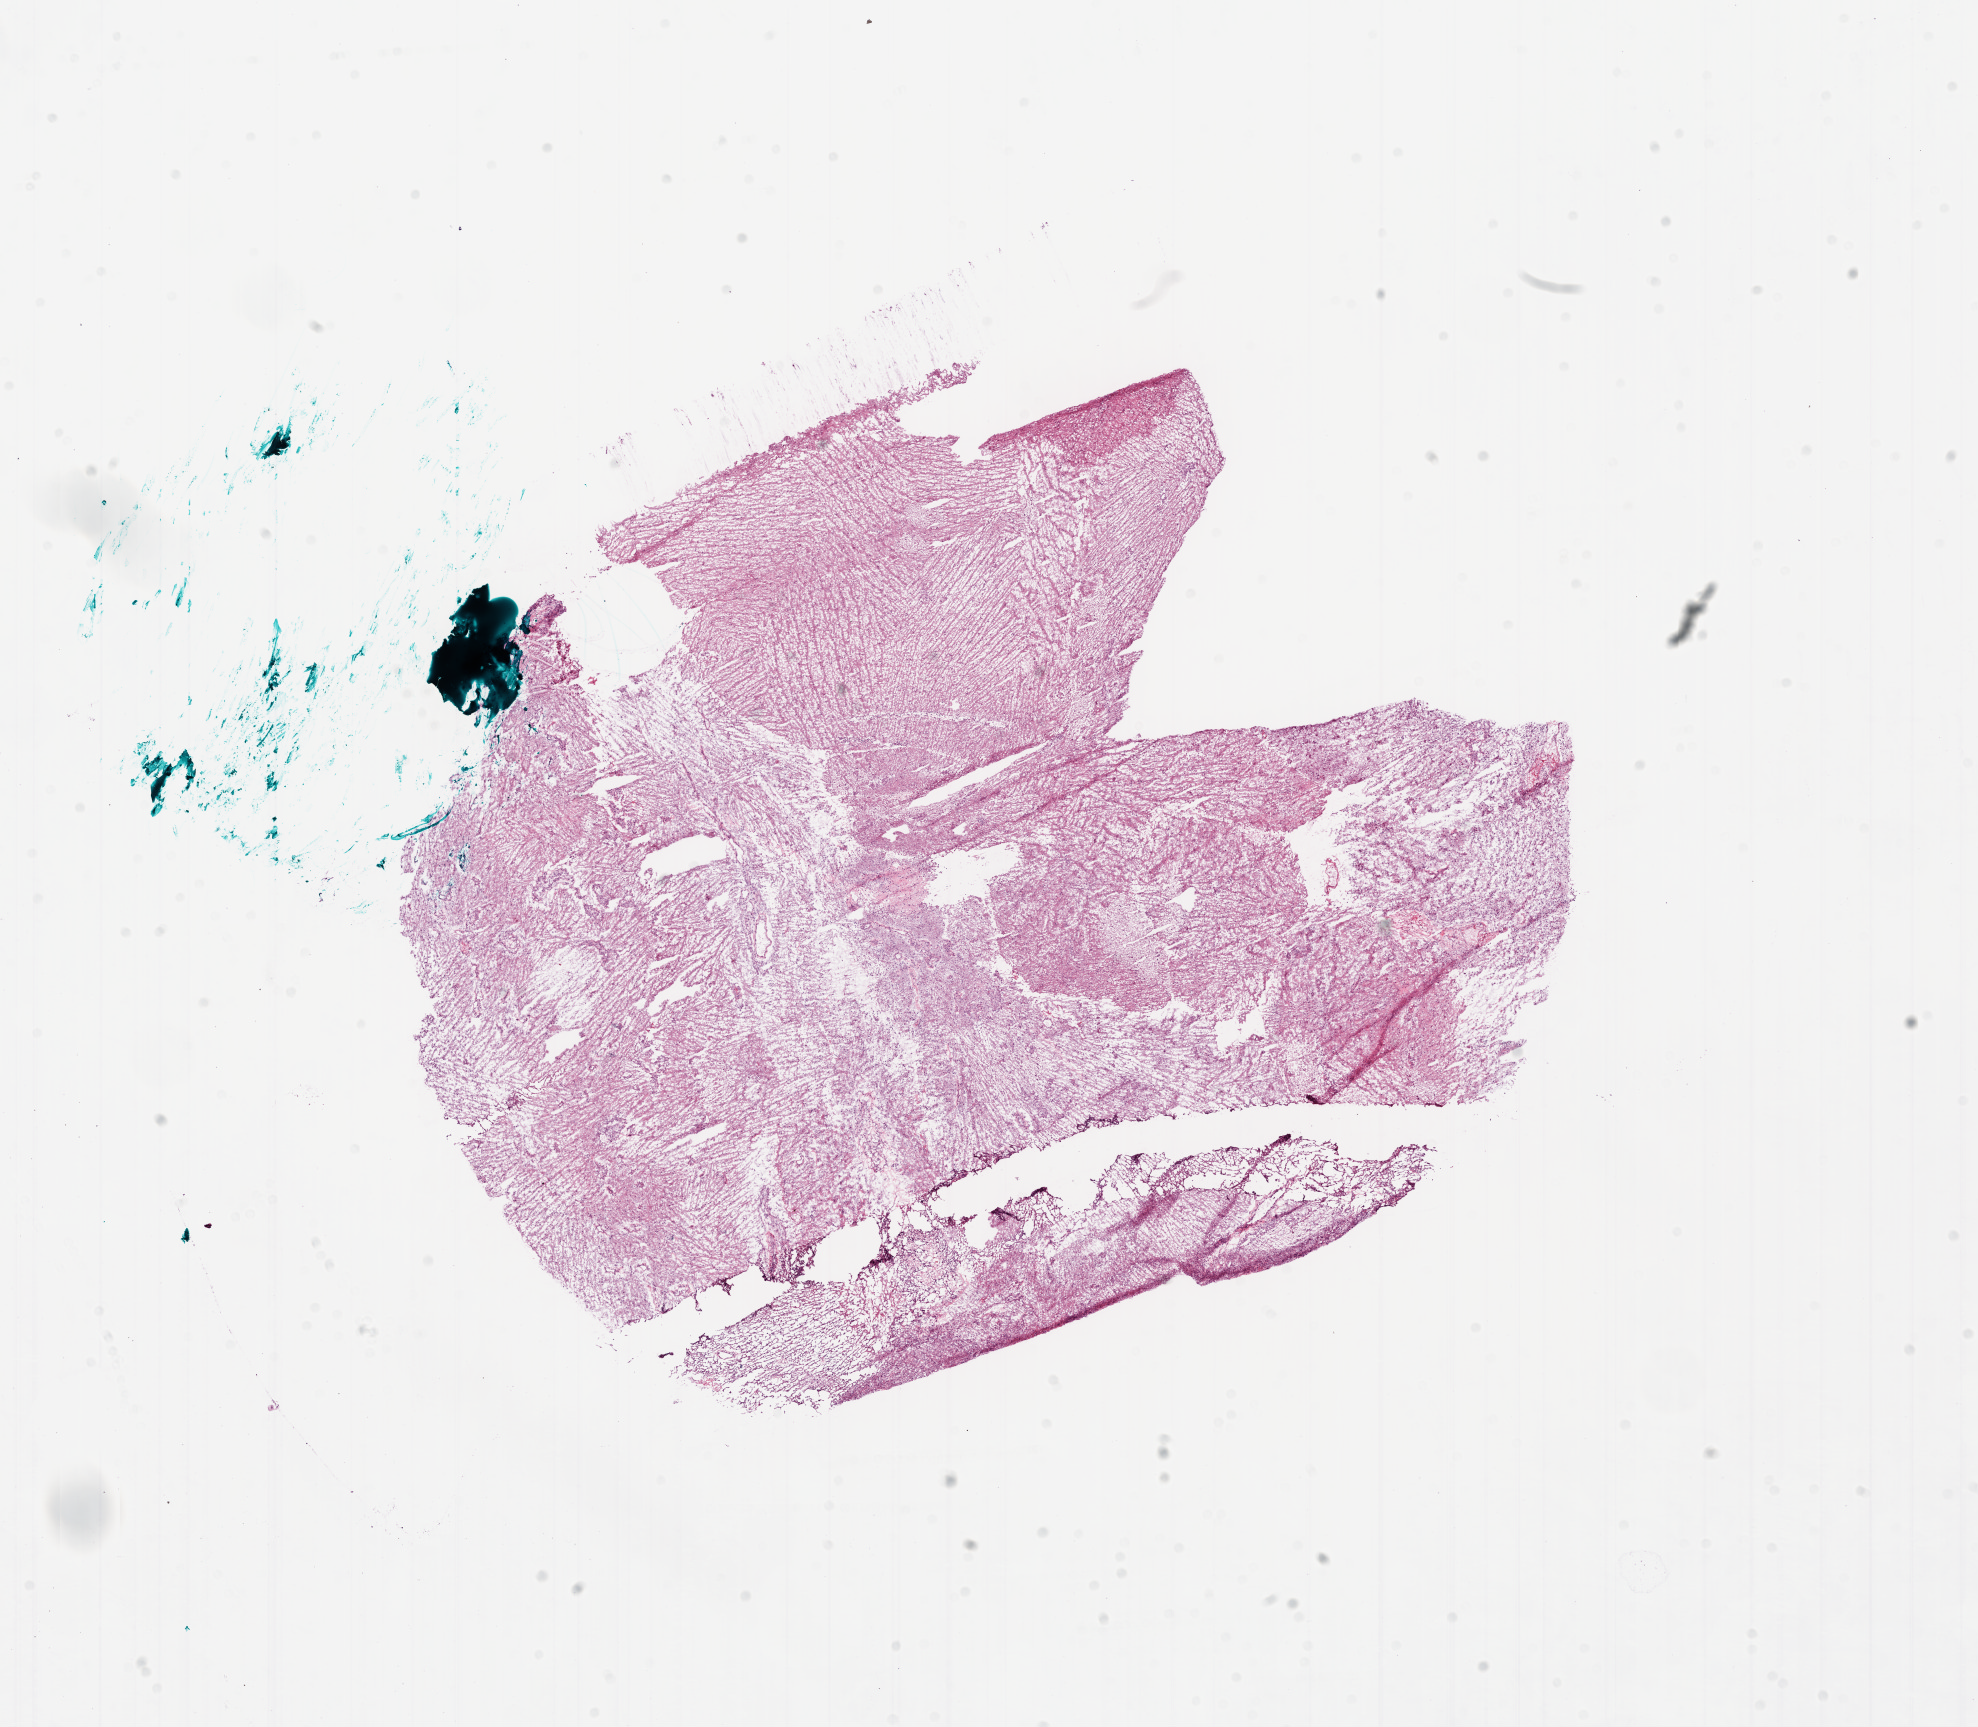
Digitized H&E tissue section (whole slide) — low-resolution overview of the scanned area, about 16.0 x 13.9 mm (from a 20x scan), frozen section from the bottom of the tissue portion, brain, primary tumour sample. Female, age 39 years at initial diagnosis. Pathologist review of this section (percent, as recorded): tumour cells 10%, tumour nuclei 60%, normal cells 0%, stromal cells 80%, necrosis 10%.
* pathologic diagnosis: Glioblastoma